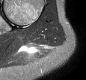
MRI of an extremity soft-tissue mass, one axial slice. Slice 21 of 30 in the series (ordered by position). STIR. MR volume resampled by the dataset authors to the PET/CT grid (not the native acquisition matrix). 86 × 80 image matrix. Female patient. From the clinical record (not read from this slice): histological type: malignant fibrous histiocytoma; grade: low; site of the primary tumour: left arm.
Outlined on this slice (expert contour drawn on MRI and transferred to this co-registered scan by the dataset authors):
- gross tumour volume (mass): bounding box (x1, y1, x2, y2) in pixels: (22, 45, 34, 52)